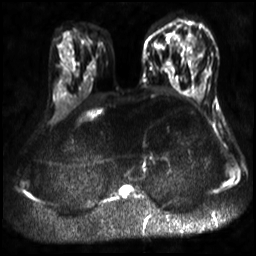
Breast MRI, one axial slice; slice 14 of 30 in the series (ordered by position); diffusion-weighted series; image 2 of 4 stored at this slice position (different b-values; order by instance number); 3 T; 4 mm slice thickness; 256 × 256 image matrix, field of view 320 × 320 mm. Female patient.
Outlined on this slice (outlined manually by an expert reader):
- tumour on diffusion-weighted imaging: bounding box <186,33,197,48> (left, top, right, bottom; pixels)